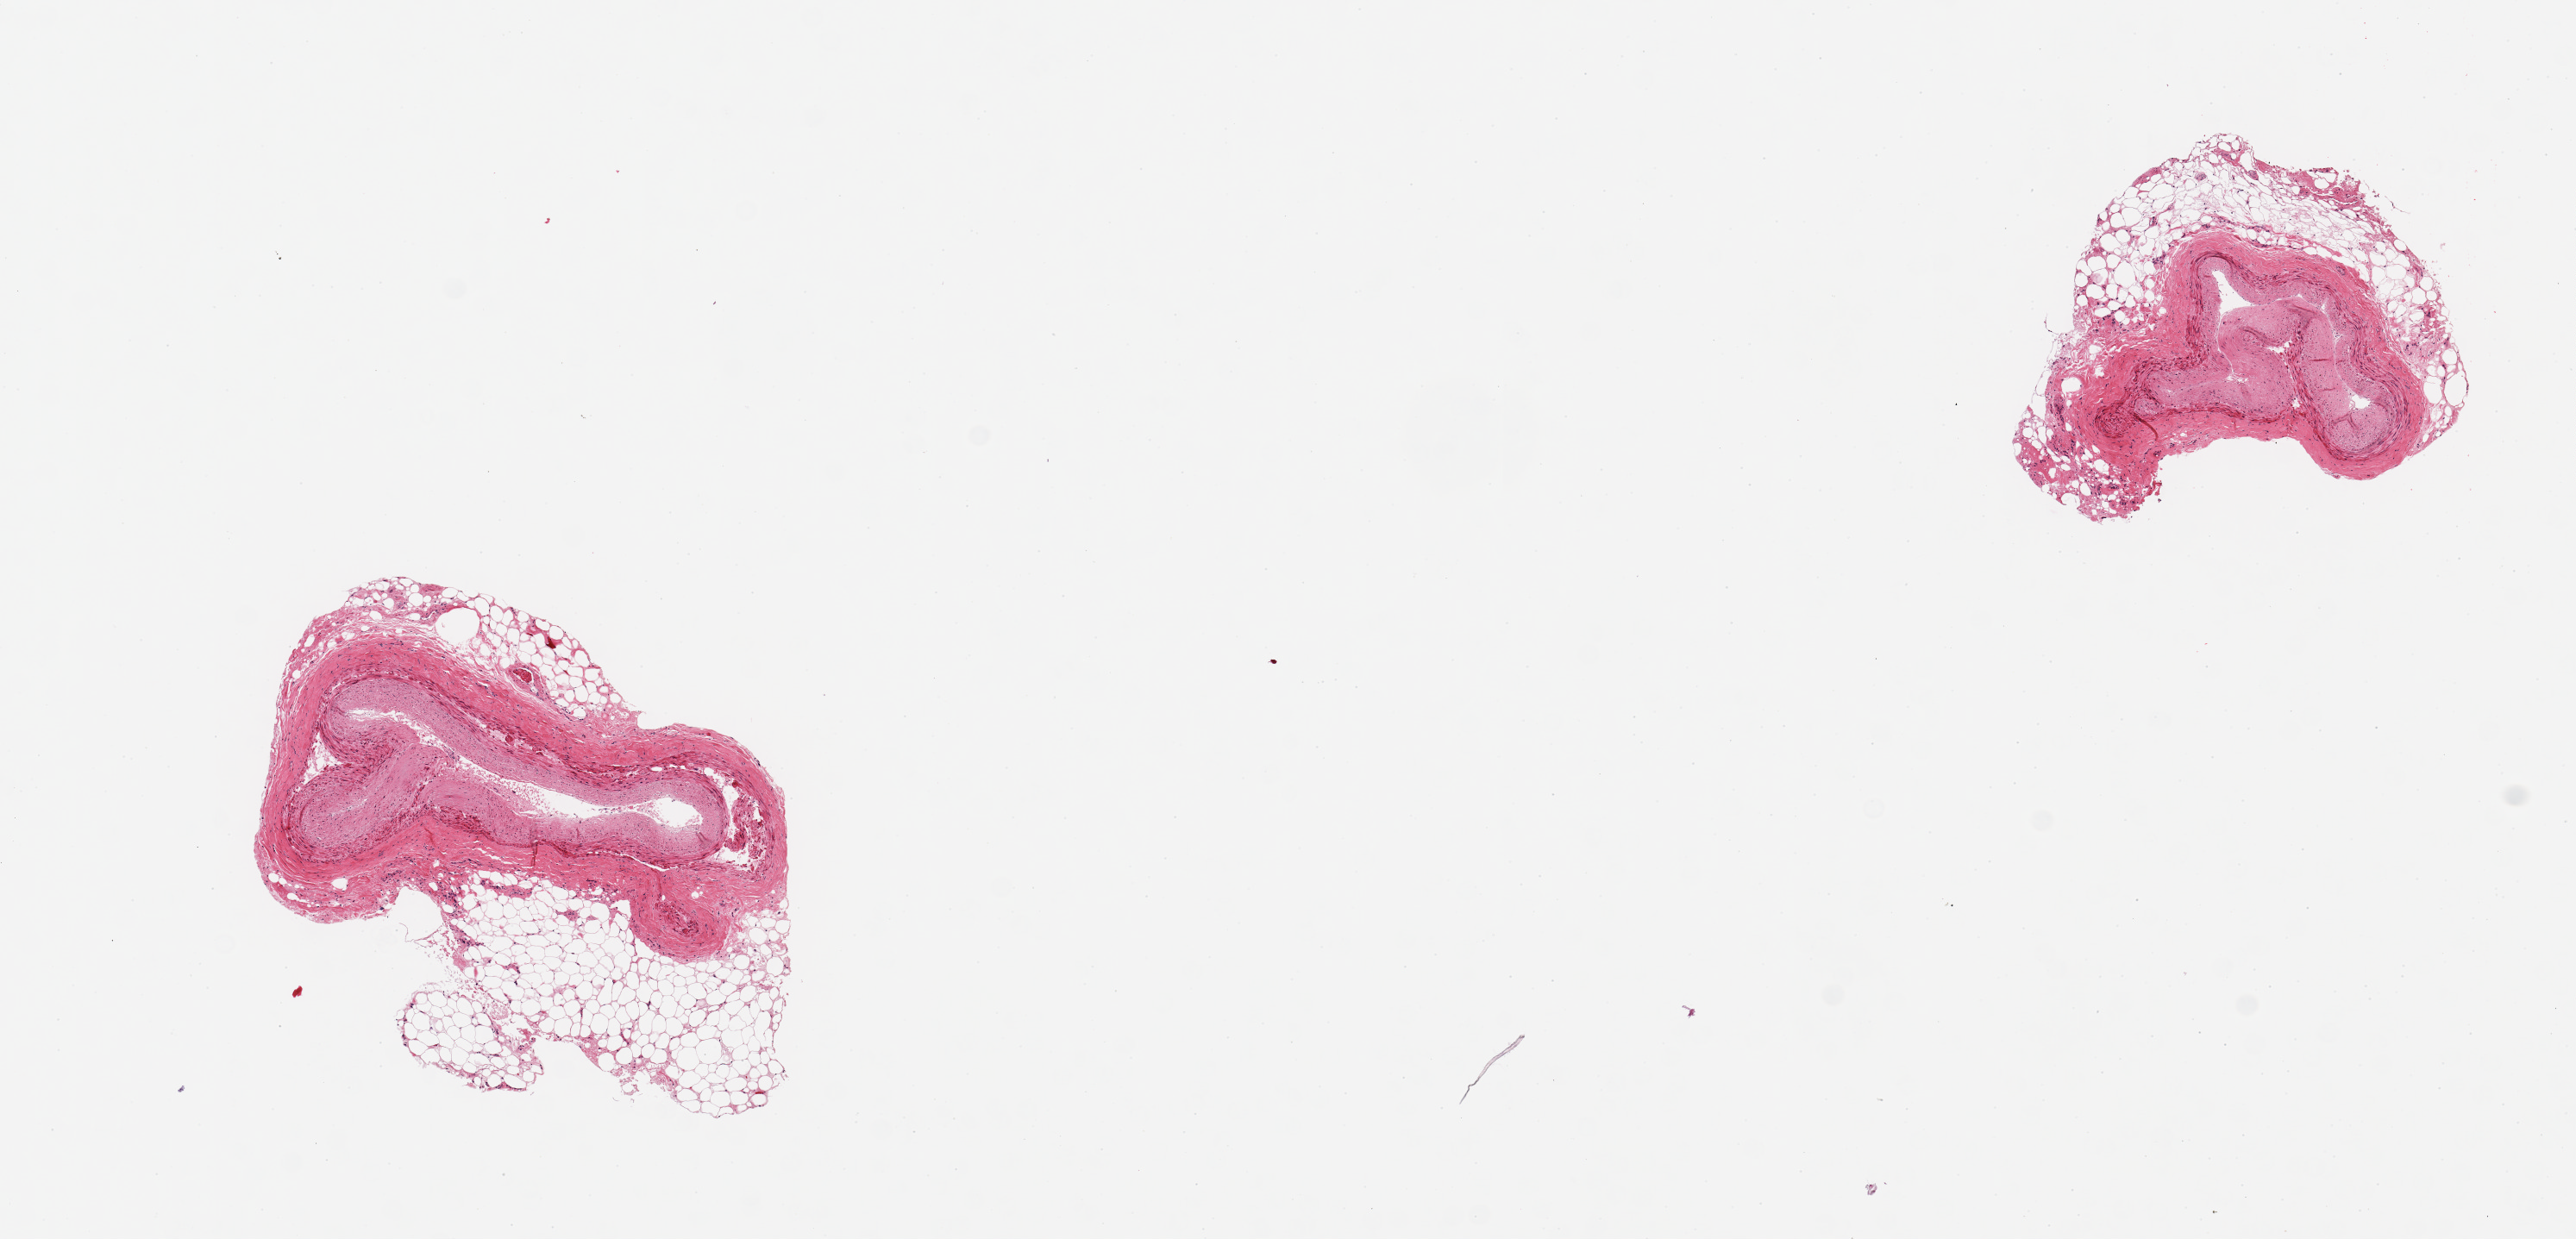
H&E whole-slide image, shown as a low-resolution overview of the whole scanned area (about 11.8 x 5.7 mm, from a 20x scan), PAXgene-fixed paraffin-embedded (PFPE) section, section of coronary artery (target tissue), tissue donor sample. Donor: female.
* reviewer comment on this tissue sample: 2 pieces; moderate fibrofatty plaque; 30% external untrimmed fat